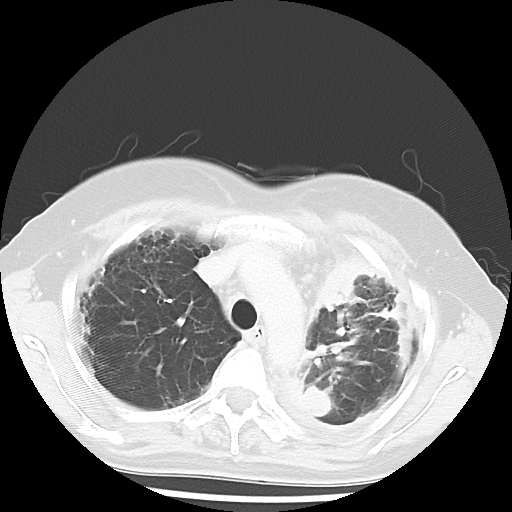
Chest CT, one axial slice. Slice 42 of 56 in the series (ordered by position). Reconstruction kernel LUNG. Lung window (W 1500 / L -600 HU). 5 mm slice thickness. 512 × 512 image matrix, field of view 309 × 309 mm. Patient: female, 56 years. Case-level facts recorded for this patient, not image findings: clinical TNM (as recorded): T1c N0 M1.
Outlined on this slice (bounding box drawn by a radiologist):
- lung tumour (recorded histology: adenocarcinoma): bounding box [x1, y1, x2, y2] px = [307, 262, 373, 327]